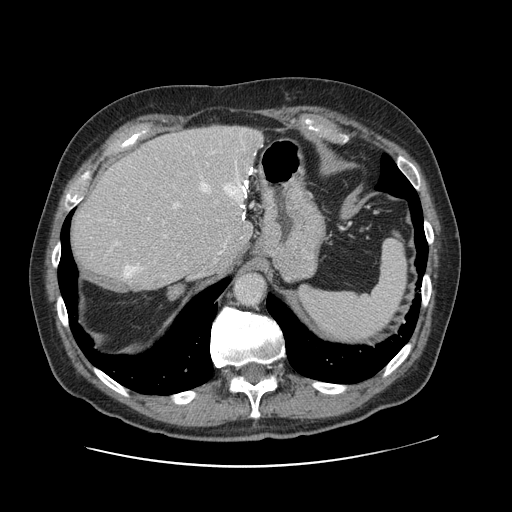
Contrast-enhanced abdominal CT, one axial slice; position 89 of 138 along the scan axis; 120 kVp; intravenous contrast given; soft-tissue window (W 400 / L 40 HU); 2.5 mm slice thickness; 512 × 512 image matrix, field of view 402 × 402 mm. Male patient, age 71 years. Case-level facts recorded for this patient, not image findings: diagnosis: colorectal cancer liver metastases, imaged before liver resection; multiple liver metastases: no; largest metastasis: 3.3 cm.
Annotated regions visible in this slice (expert manual segmentation):
- hepatic veins: bounding box [x1, y1, x2, y2] px = [124, 181, 248, 278]
- liver: [71, 126, 262, 291]
- planned liver remnant (the part of the liver to remain after resection): [71, 154, 242, 291]
- portal vein (with intrahepatic branches): [114, 202, 181, 245]